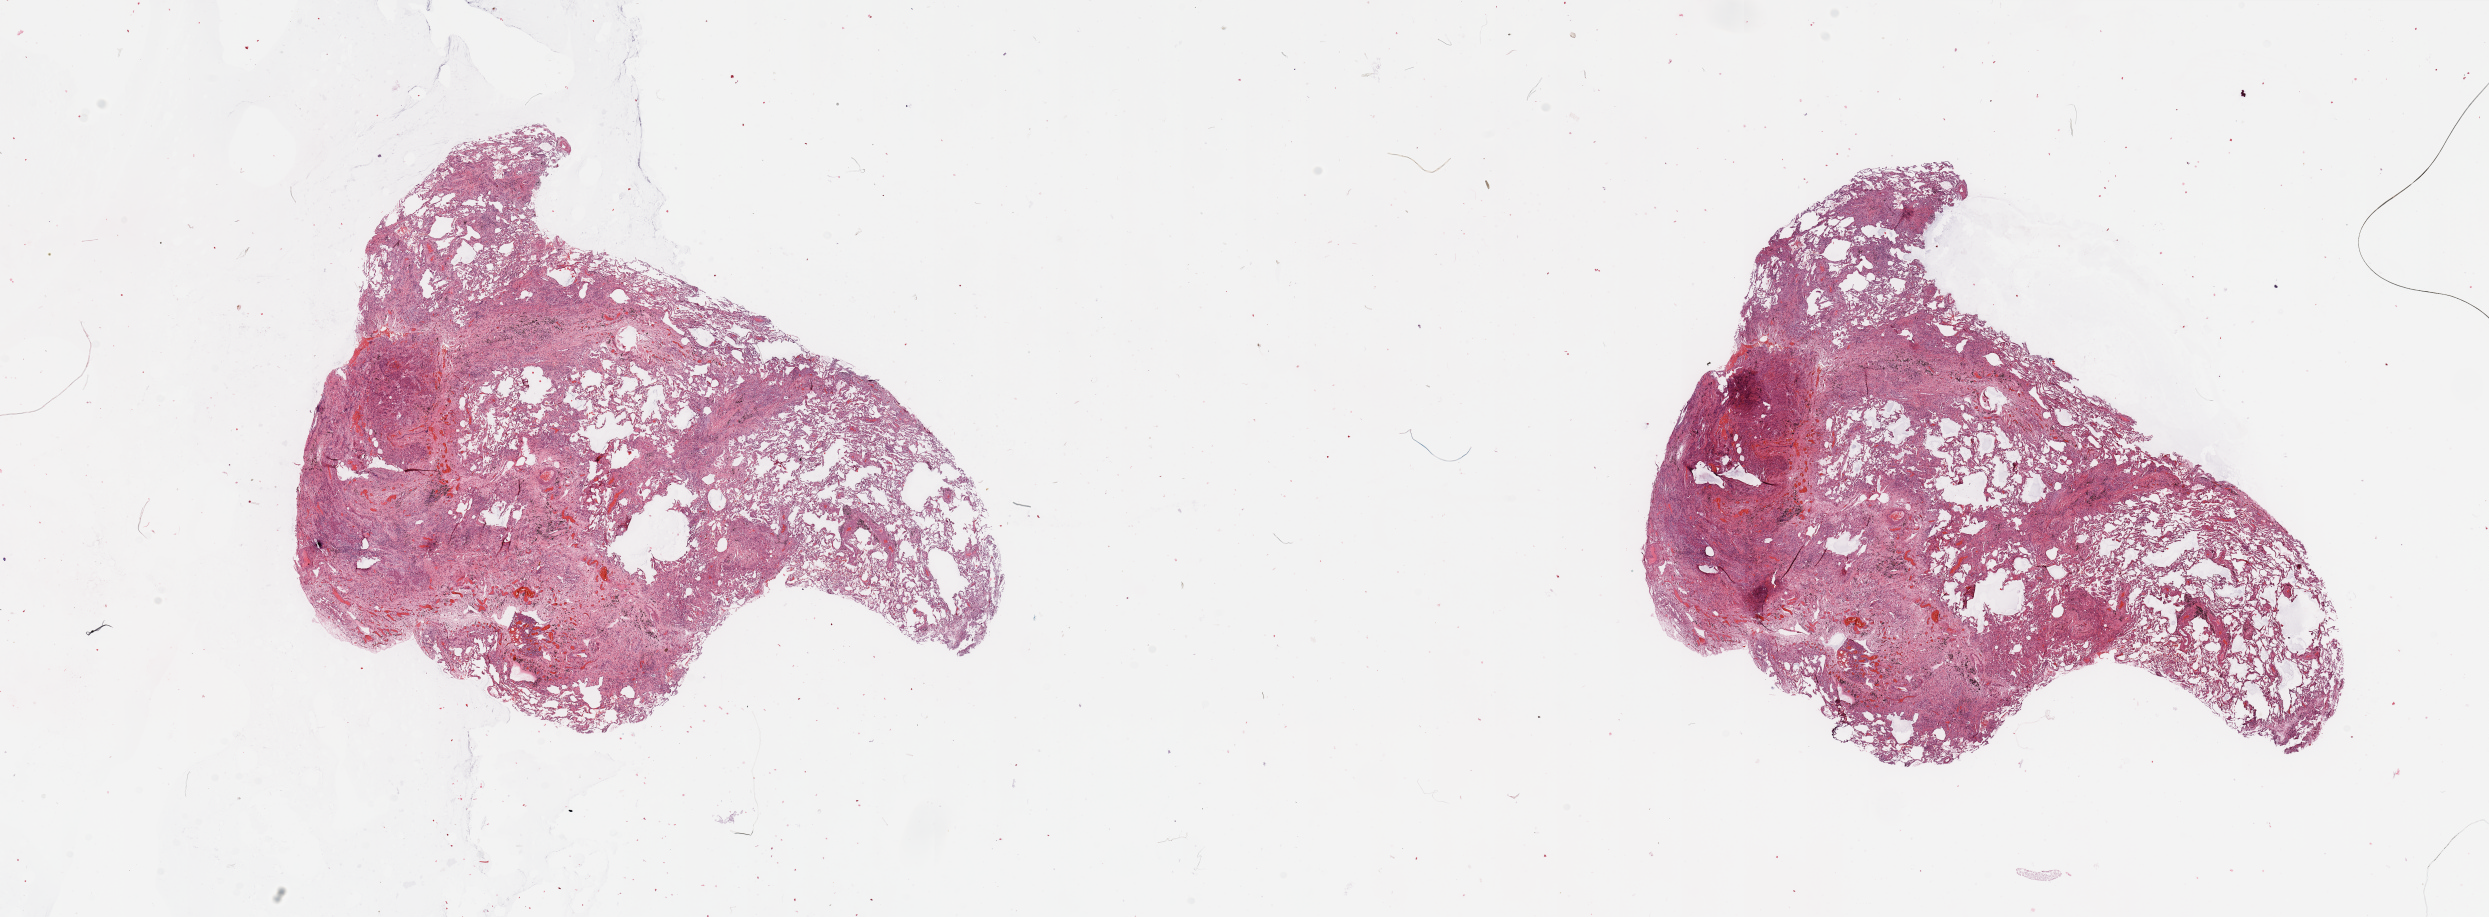
Whole-slide histology image, H&E-stained, a low-resolution overview of the entire scanned area, about 39.4 x 14.5 mm. Lung, normal (non-tumour) tissue. Male, 65 y/o.
This section: normal (non-tumour) tissue from the same patient. Patient diagnosis: Adenocarcinoma, NOS.